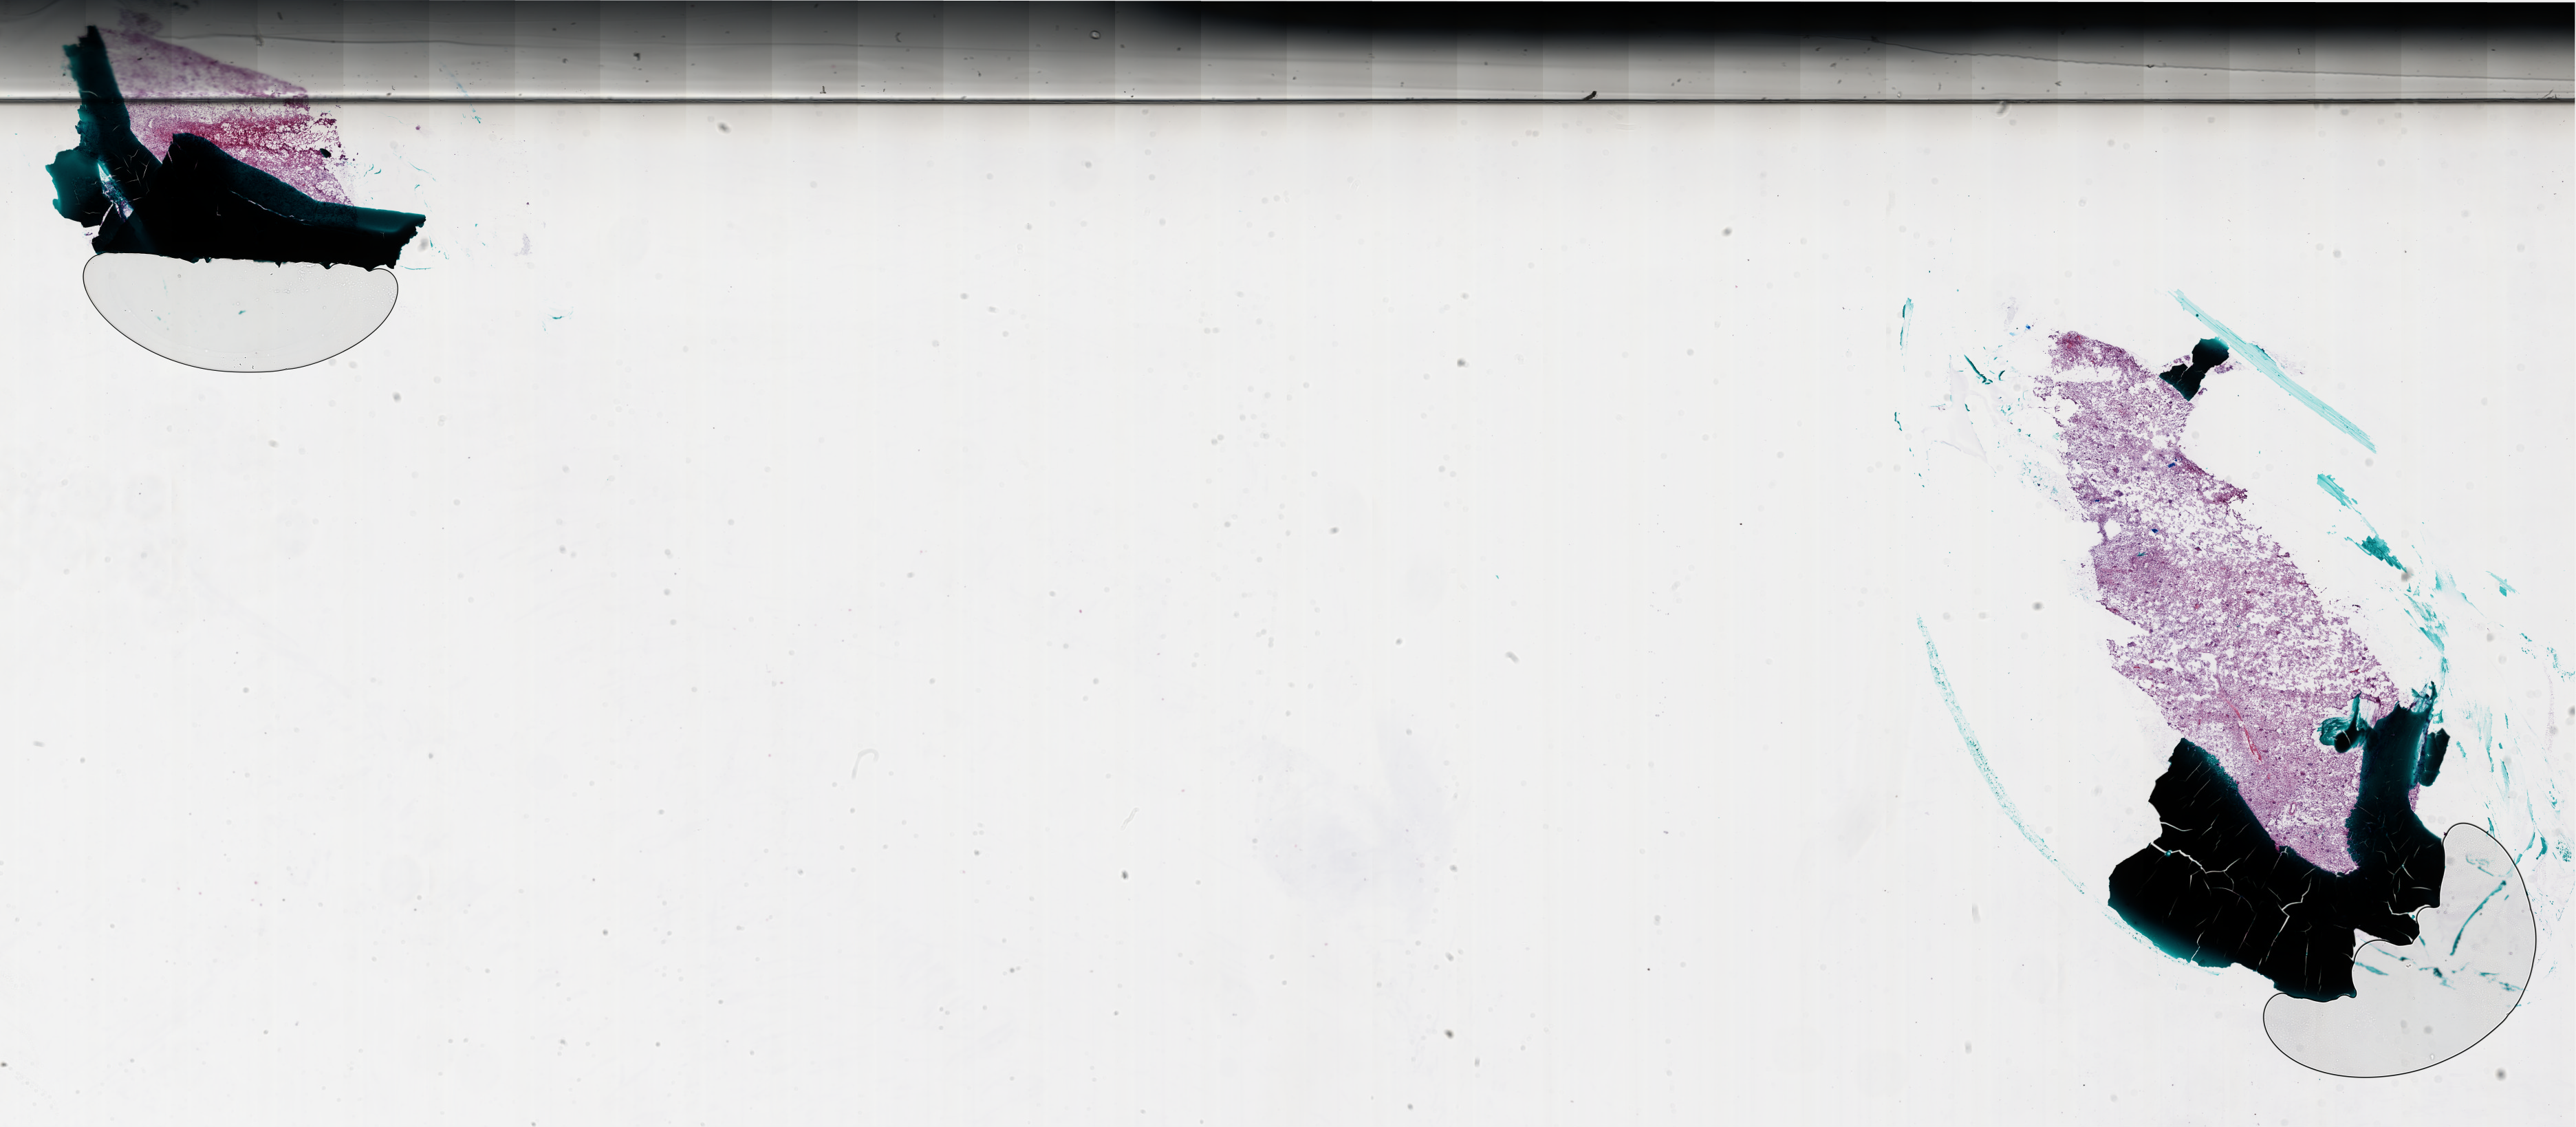
Digitized H&E tissue section (whole slide), whole scanned area (about 30.0 x 13.1 mm) shown as a low-resolution overview; frozen section from the bottom of the tissue portion; sample: primary tumour, brain. Patient: female, age at initial diagnosis 55 years.
Histologic diagnosis: Glioblastoma.